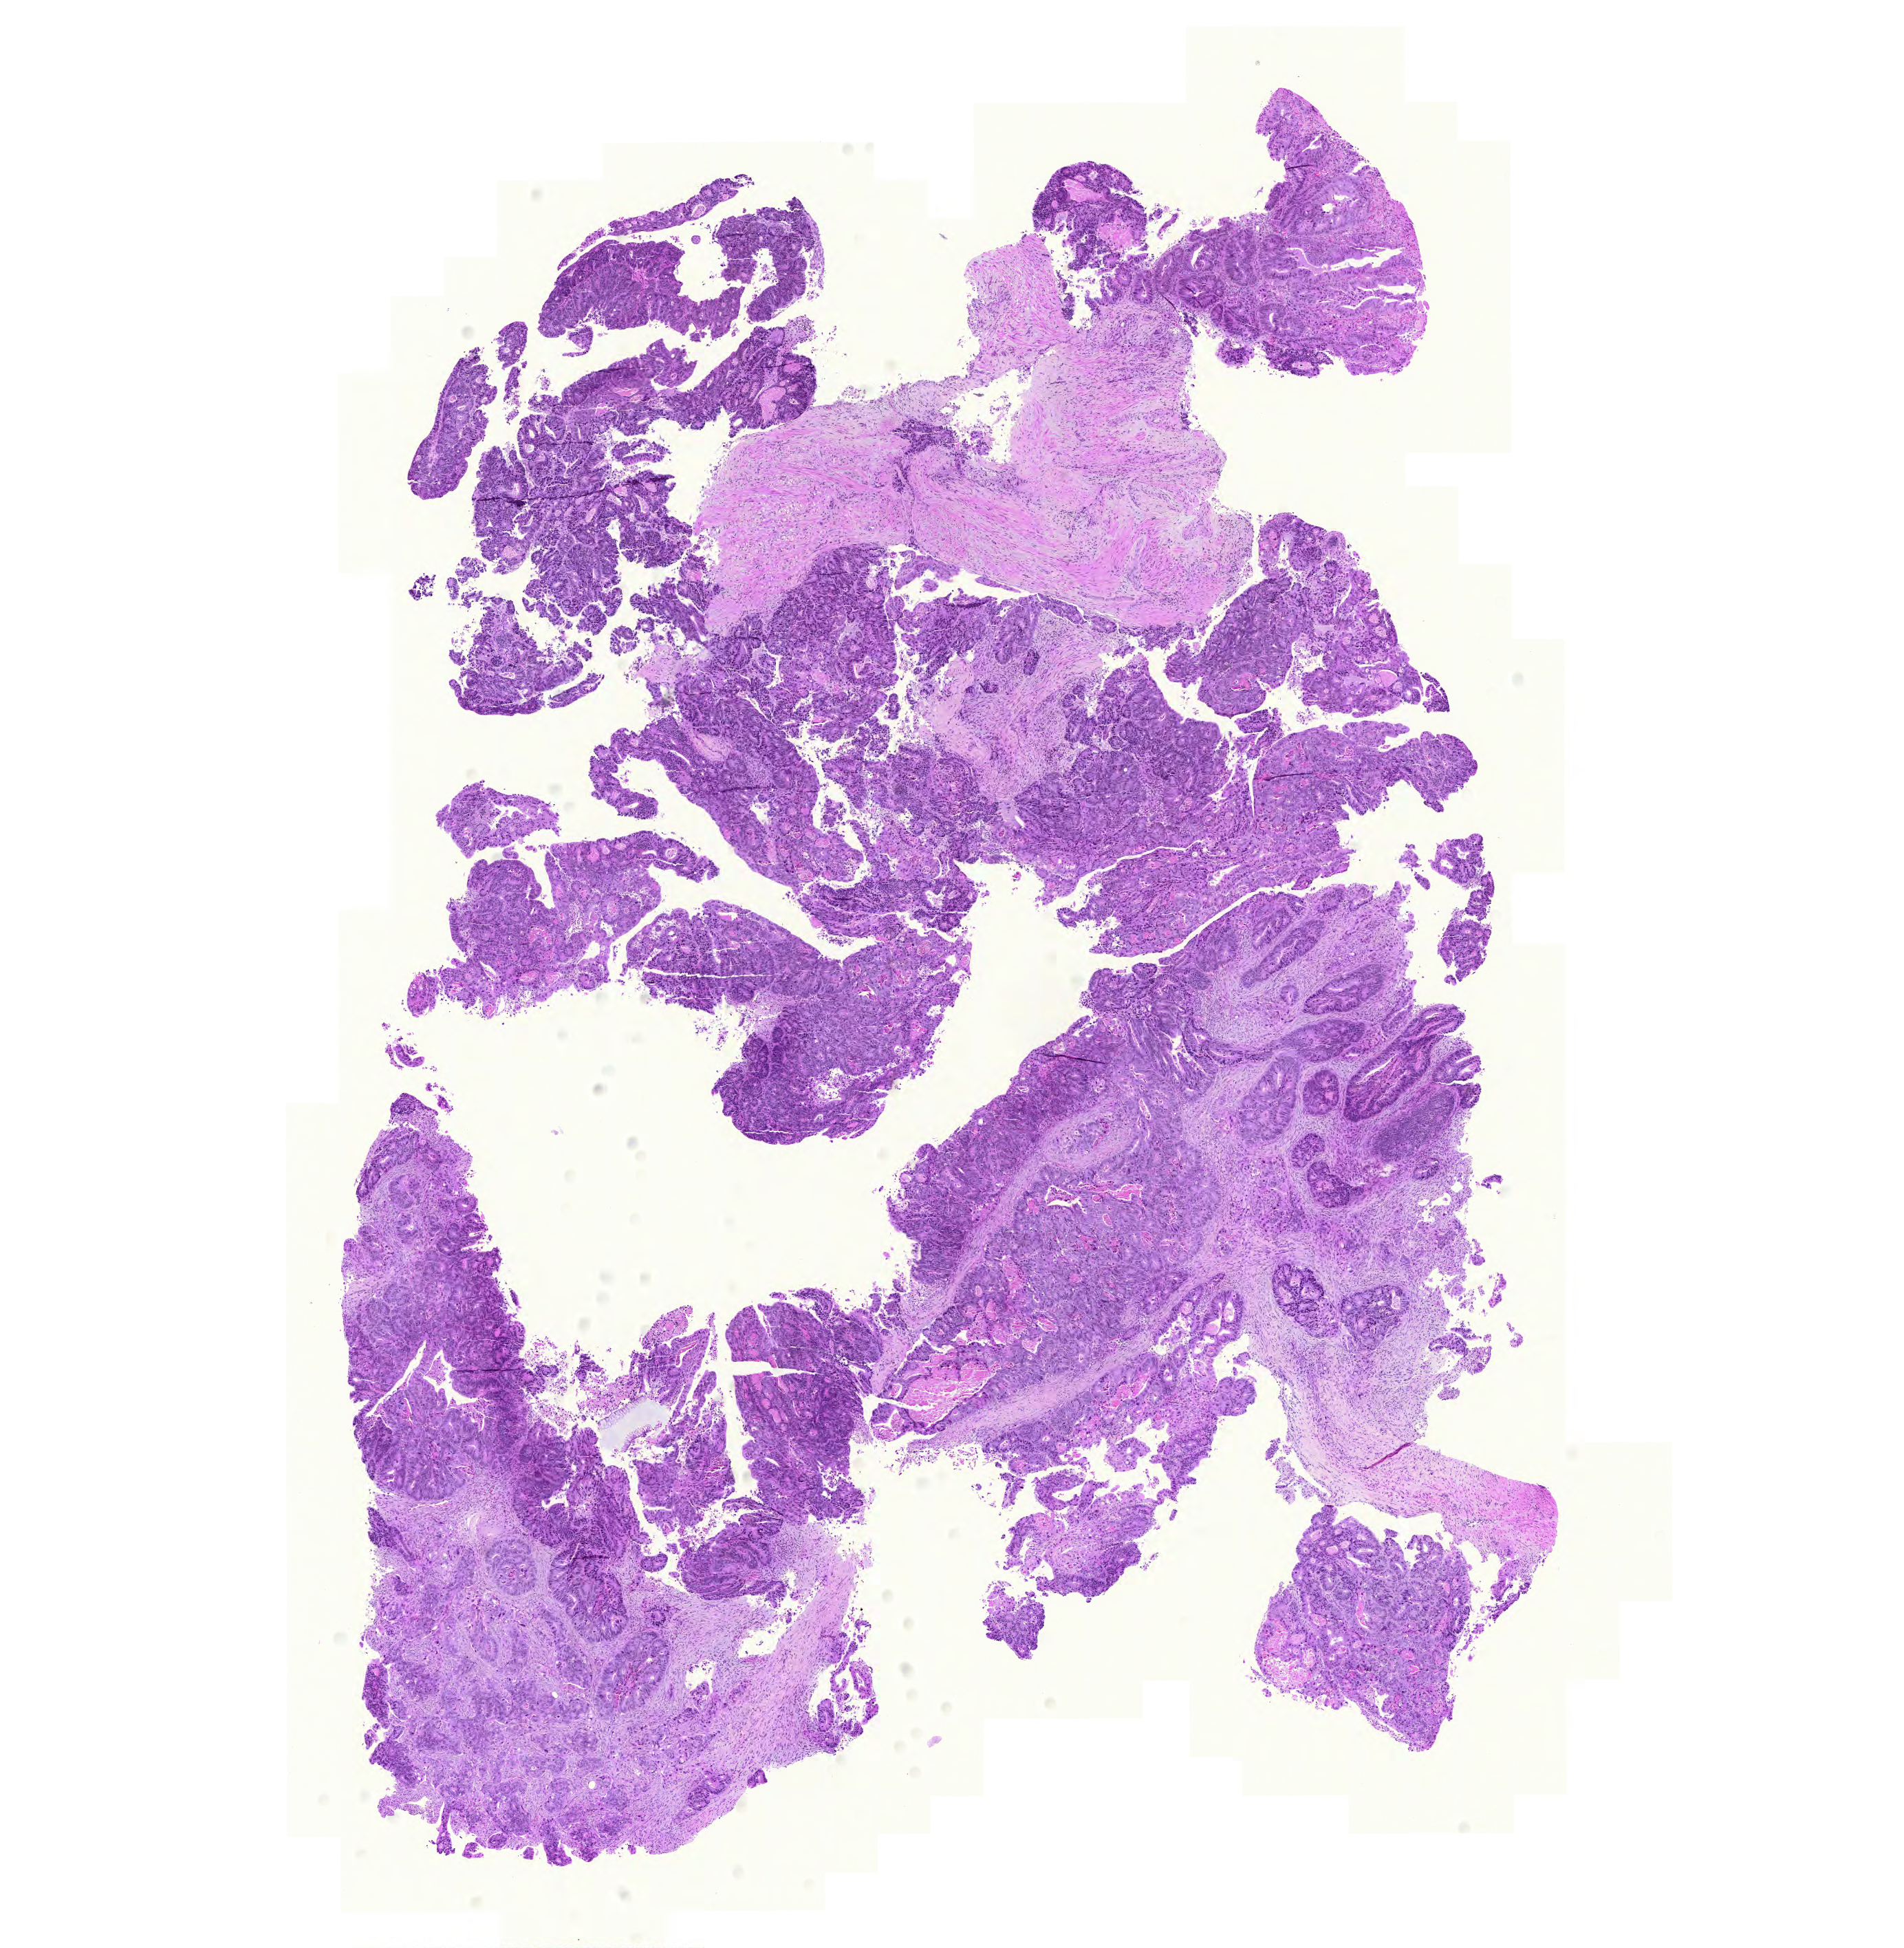
Digitized H&E-stained tissue section (whole slide), low-resolution overview of the scanned area, about 10.3 x 10.5 mm (slide scanned at 20x); formalin-fixed paraffin-embedded (FFPE) diagnostic section; colon, primary tumour sample. Male, age 77 years at initial diagnosis.
Pathologic diagnosis: Adenocarcinoma, NOS.